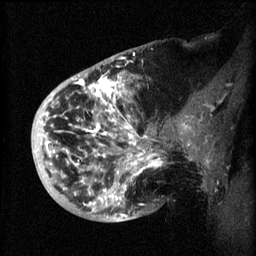
Breast MRI (dynamic contrast-enhanced), one sagittal slice. Position 18 of 60 along the scan axis. 3 images stored at this slice position (order not interpretable as contrast timing). 1.5 T. TE 4.2 ms, TR 8.2 ms. 2 mm slice thickness. 256 × 256 image matrix, field of view 200 × 200 mm. Female patient, age 50 years.
Outlined on this slice (semi-automatic segmentation, software-assisted and operator-edited):
- analysis volume of interest (the breast-tissue region the enhancement analysis was run in; not a lesion): bounding box [x1, y1, x2, y2] px = [44, 72, 173, 219]
- tumour enhancement mask (voxels above the 70 % enhancement threshold inside the analysis volume of interest): [44, 76, 164, 217]